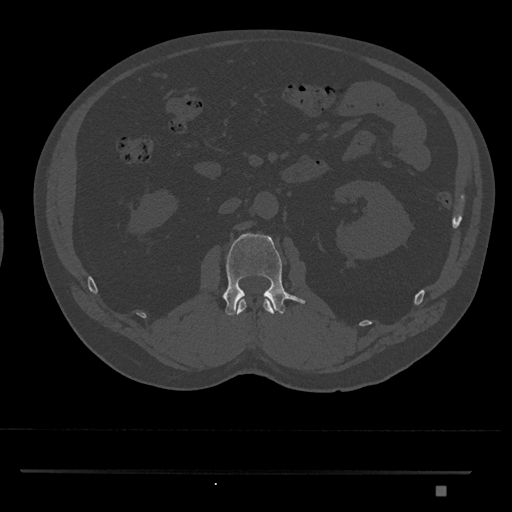
CT including the spine, one axial slice. Slice 770 of 1134 in the series (ordered by position). Reconstruction kernel Br40s/3. Bone window (W 1800 / L 400 HU). 0.5 mm slice thickness. 512 × 512 image matrix. Male patient, age 65 years. From the clinical record (not read from this slice): primary cancer: prostate.
Outlined on this slice (semi-automatic segmentation, software-assisted and operator-edited):
- L1 vertebra: bounding box (x1, y1, x2, y2) in pixels: (236, 299, 275, 315)
- L2 vertebra: (222, 233, 306, 316)